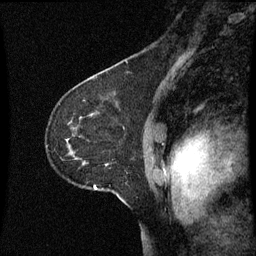
Breast MRI (dynamic contrast-enhanced), one sagittal slice. Position 43 of 60 along the scan axis. Dynamic contrast-enhanced series, image 2 of 3 at this slice position (ordered by acquisition). 1.5 T. TE 4.2 ms, TR 8.9 ms. 2 mm slice thickness. 256 × 256 image matrix, field of view 200 × 200 mm. Female patient, age 53 years. Case-level facts recorded for this patient, not image findings: setting: breast cancer imaged before/during neoadjuvant chemotherapy; receptor status: HR-positive, HER2-negative.
Annotated regions visible in this slice (semi-automatically segmented with operator editing):
- analysis volume of interest (the breast-tissue region the enhancement analysis was run in; not a lesion): bounding box <46,86,149,207> (left, top, right, bottom; pixels)
- tumour enhancement mask (voxels above the 70 % enhancement threshold inside the analysis volume of interest): <94,186,97,189>